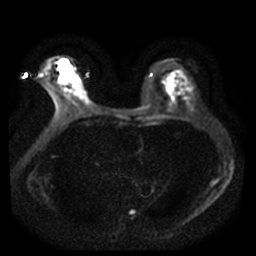
Breast MRI, one axial slice; slice 21 of 42 in the series (ordered by position); diffusion-weighted series; image 2 of 4 stored at this slice position (different b-values; order by instance number); 3 T; 5 mm slice thickness; 256 × 256 image matrix, field of view 340 × 340 mm. Female patient.
Structures marked on this image (expert manual segmentation):
- tumour on diffusion-weighted imaging: bounding box (x1, y1, x2, y2) in pixels: (60, 61, 72, 74)